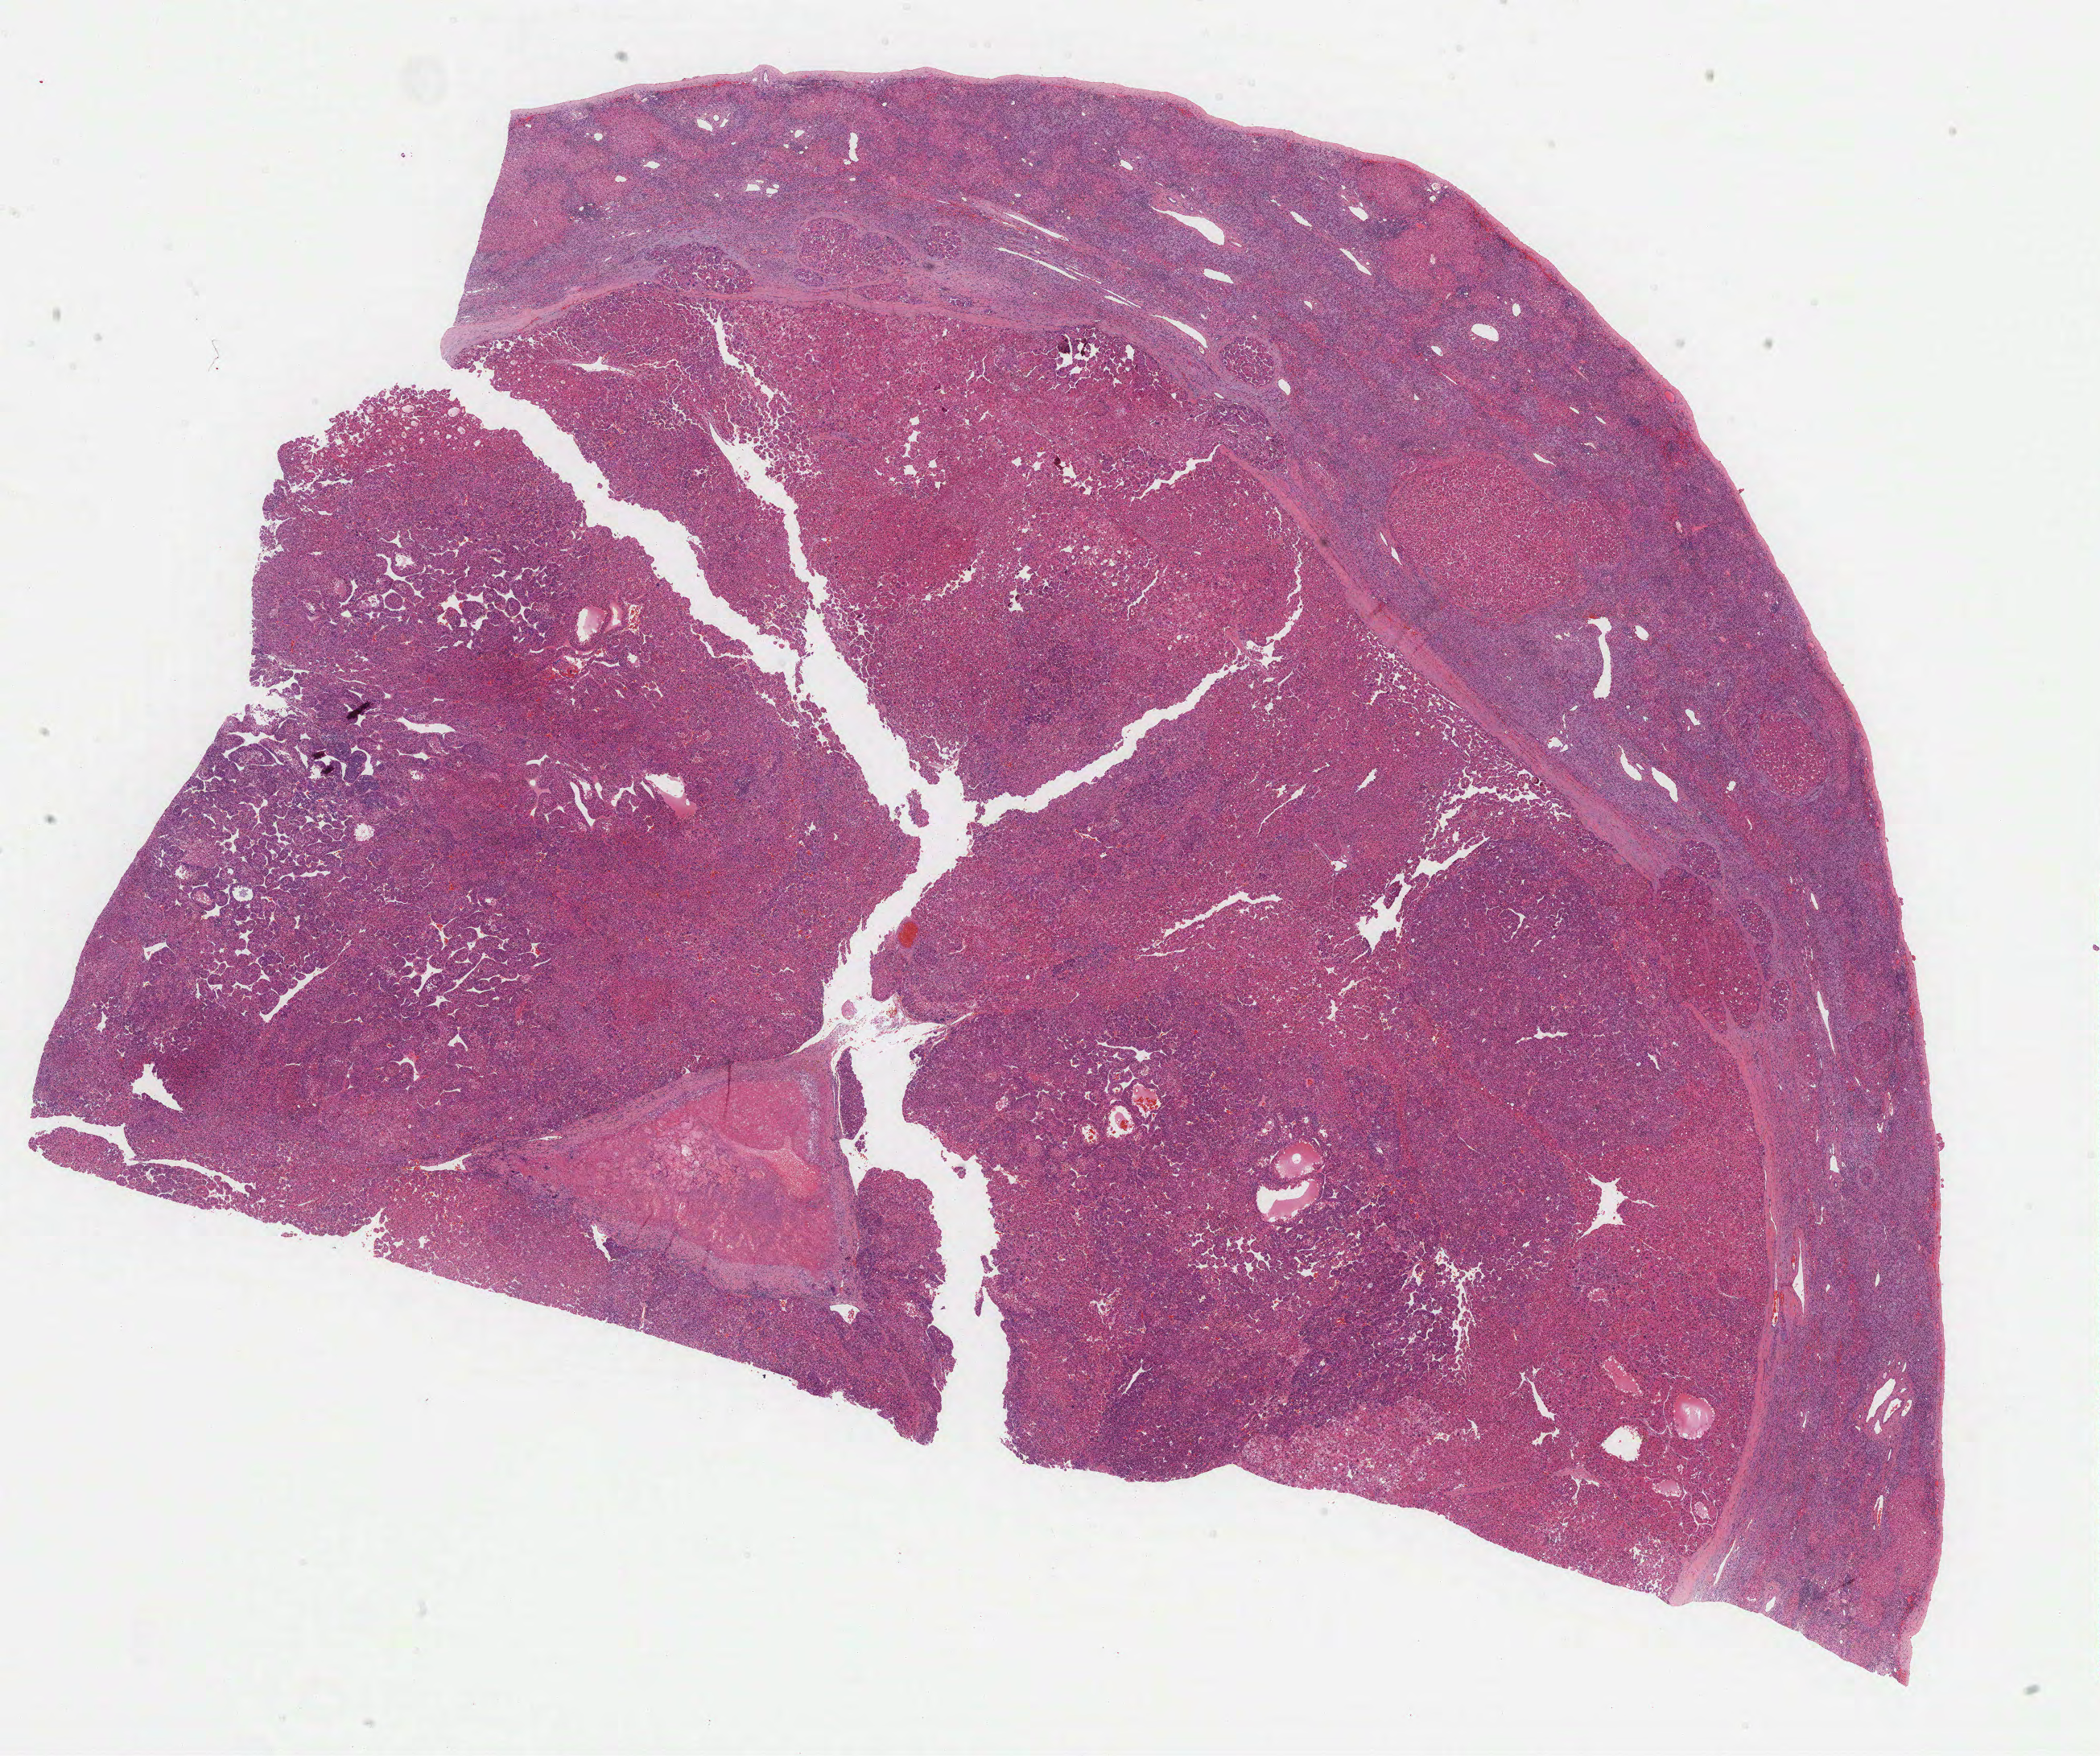
Digitized Hematoxylin and eosin (H&E) stained tissue section (whole slide) — shown as a low-resolution overview of the whole scanned area (about 21.1 x 17.6 mm, from a 40x scan). FFPE section. Primary tumour sample from the liver. Patient: male, age at initial diagnosis 70 years. Histologic grade: G2 (moderately differentiated).
TNM: T2 NX MX. Pathologic diagnosis: Hepatocellular carcinoma, NOS. AJCC pathologic stage: II.